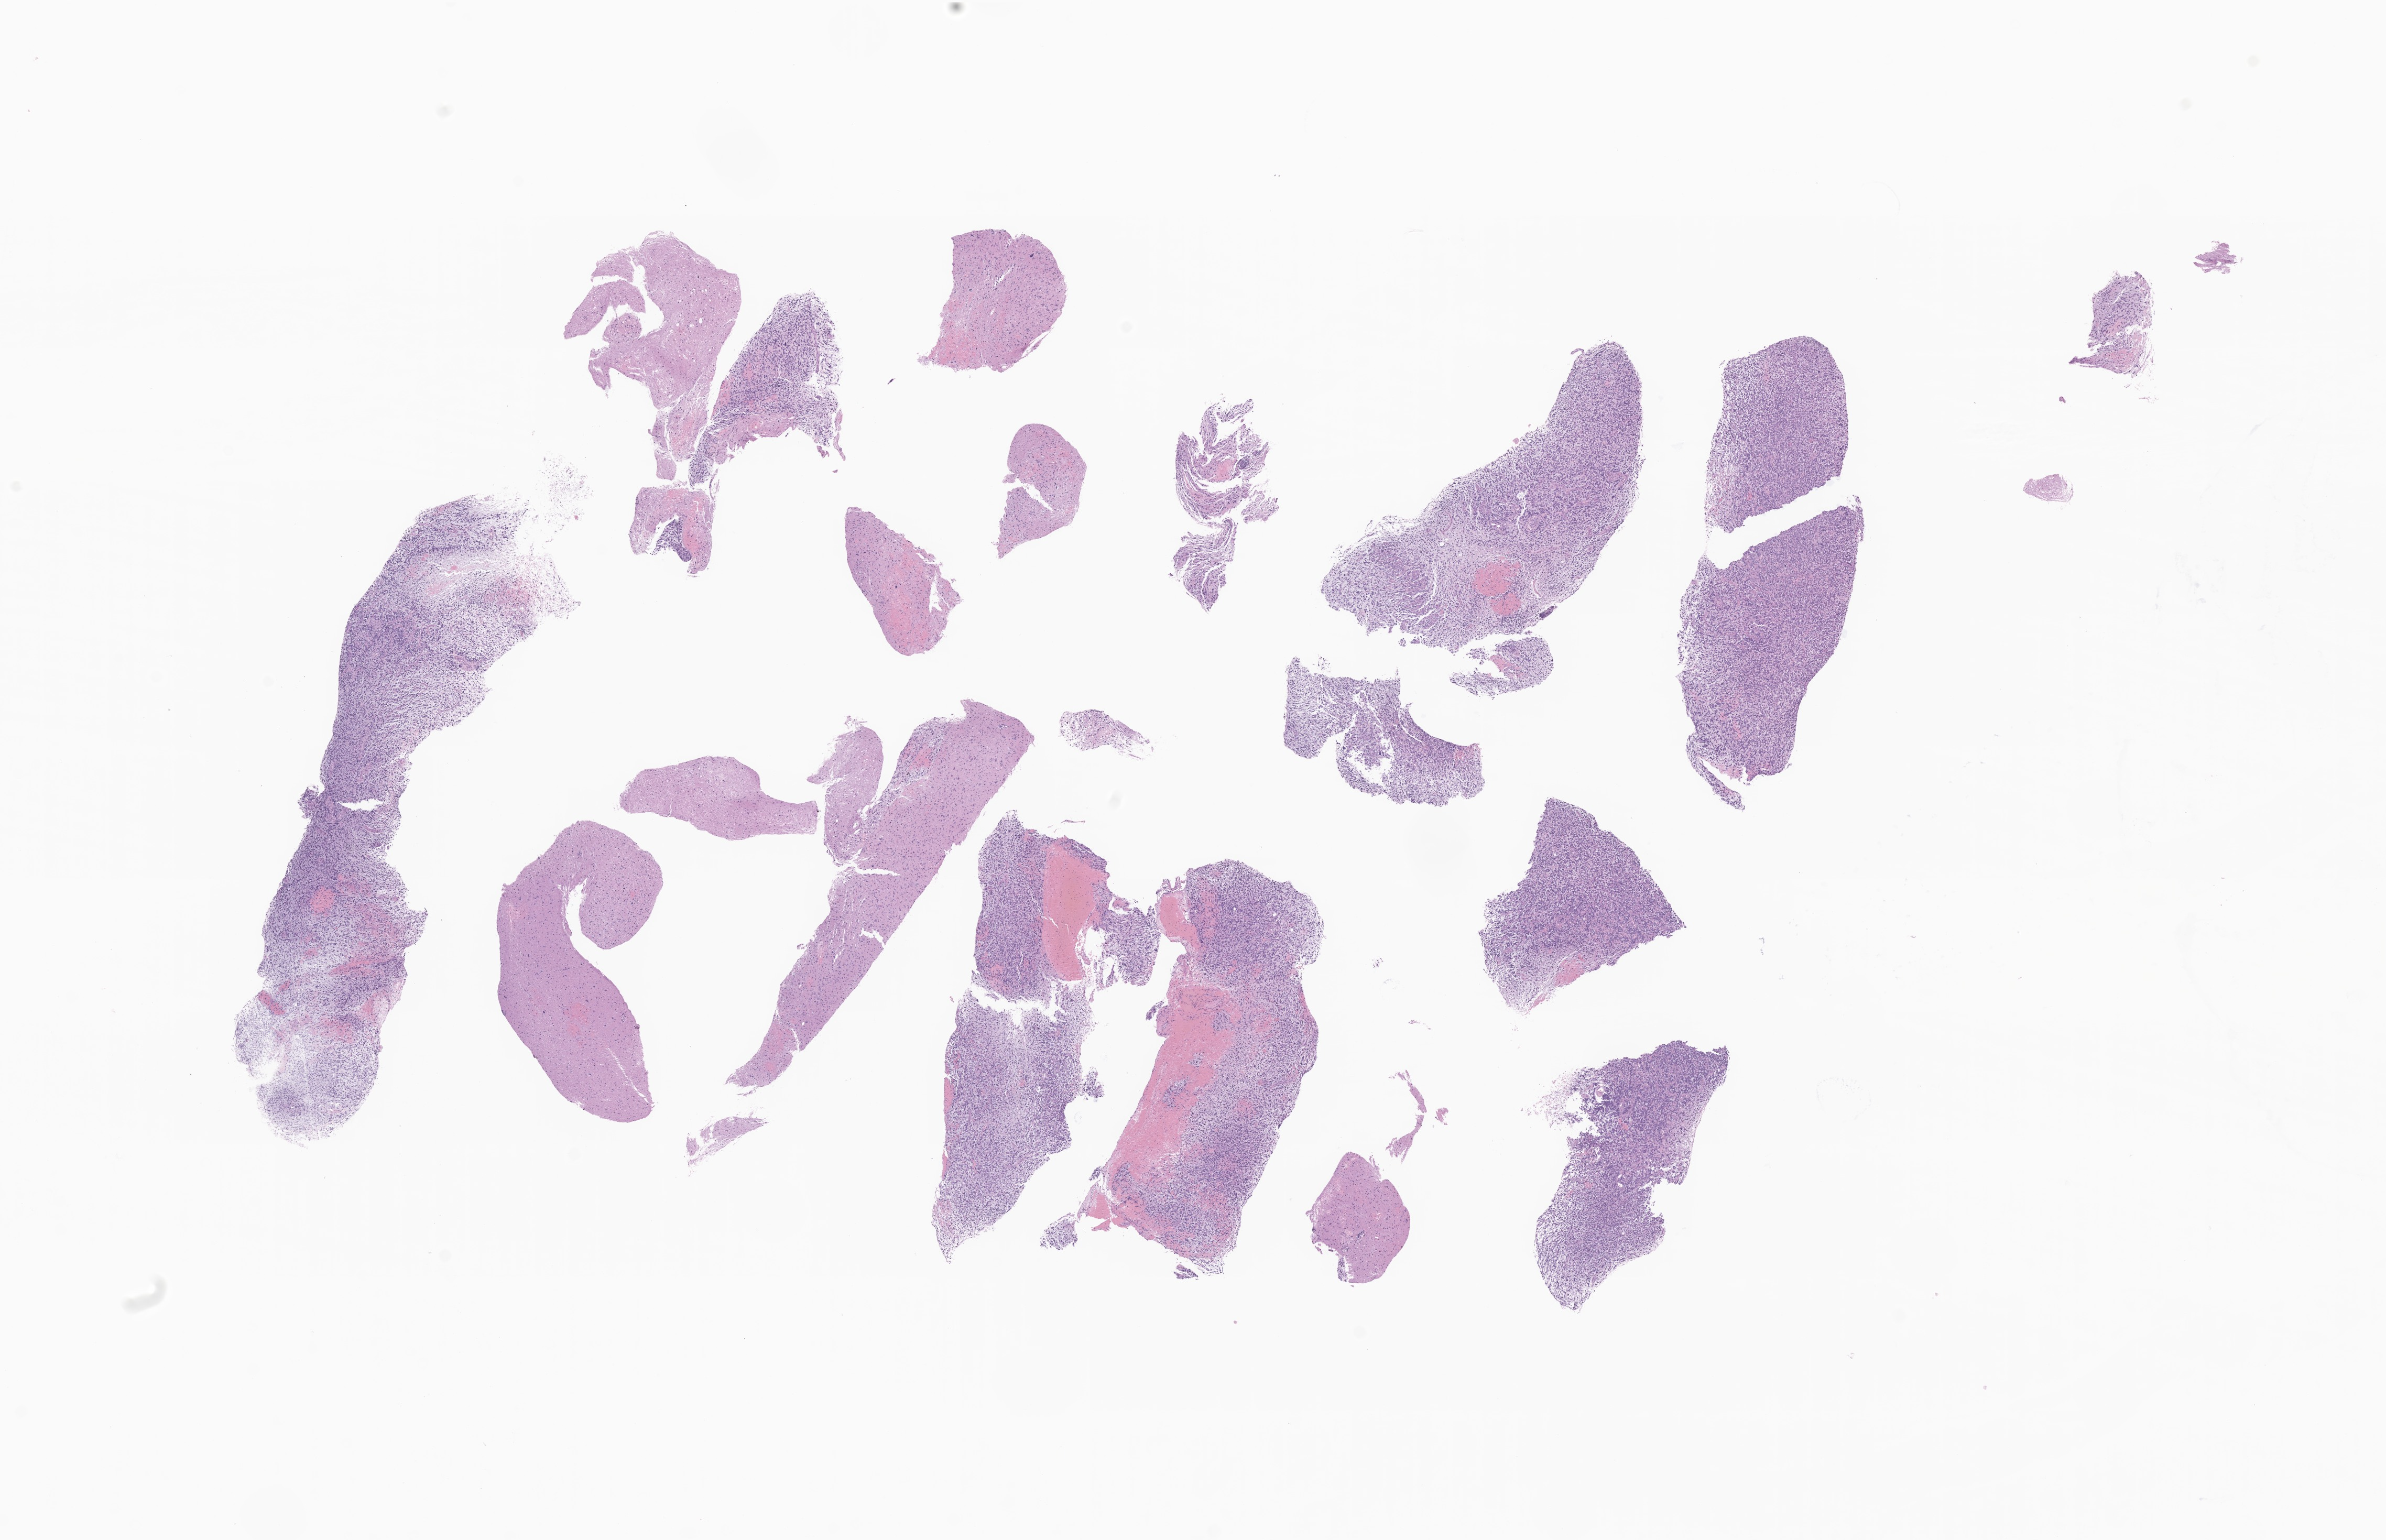
Digitized haematoxylin and eosin-stained section of tumor tissue from the brain, shown as a low-resolution overview of the whole scanned area (about 19.2 x 12.4 mm). FFPE section. Patient: female, age 122 months (10 years 2 months).
* diagnosis (ICD-O-3 morphology term): Glioma, malignant